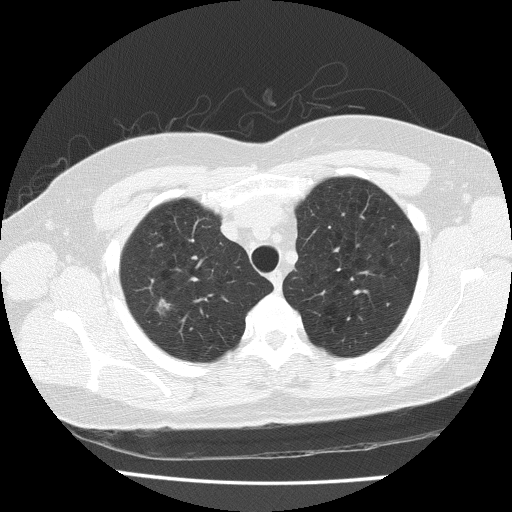
Axial slice from a low-dose chest CT screening exam; baseline annual screen; lung window (W 1500 / L -600 HU); 2 mm slice thickness; lung (sharp) reconstruction kernel (FC51); 512 × 512 image matrix. Female, age 57 years at enrolment. Former smoker at enrolment.
Lesion marked by an expert reader, bounding box [x1, y1, x2, y2] px = [136, 288, 180, 330]. Reader record for this screening exam (exam-level; its link to the box is not recorded): non-calcified nodule or mass ≥4 mm, right upper lobe, 8 × 7 mm, spiculated (stellate) margins, soft tissue attenuation. Official screen result: positive, change unspecified: nodule(s) >= 4 mm or enlarging nodule(s), mass(es), or other non-specific abnormalities suspicious for lung cancer. Later outcome: lung cancer diagnosed 132 days after this screen — bronchiolo-alveolar adenocarcinoma, NOS, right upper lobe, well differentiated (G1), stage IA (AJCC 6th edition), 12 mm at pathology.